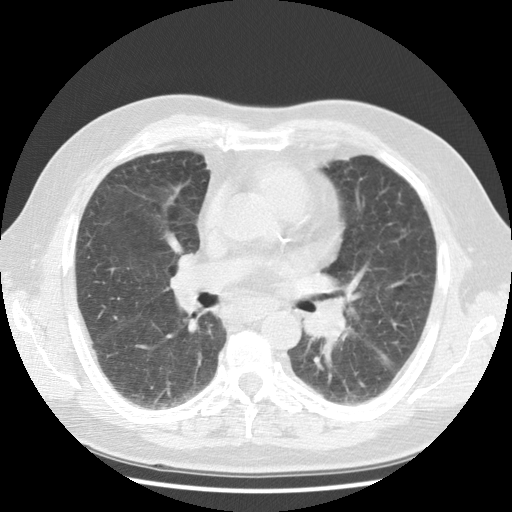
Low-dose screening chest CT, one axial slice; reconstruction kernel STANDARD; lung window (W 1500 / L -600 HU); 2.5 mm slice thickness; 512 × 512 image matrix, field of view 350 × 350 mm.
Structures marked on this image (outlined manually by an expert reader):
- lesion 1 (tumor, hilum of left lung): bounding box (x1, y1, x2, y2) in pixels: (304, 297, 347, 343)